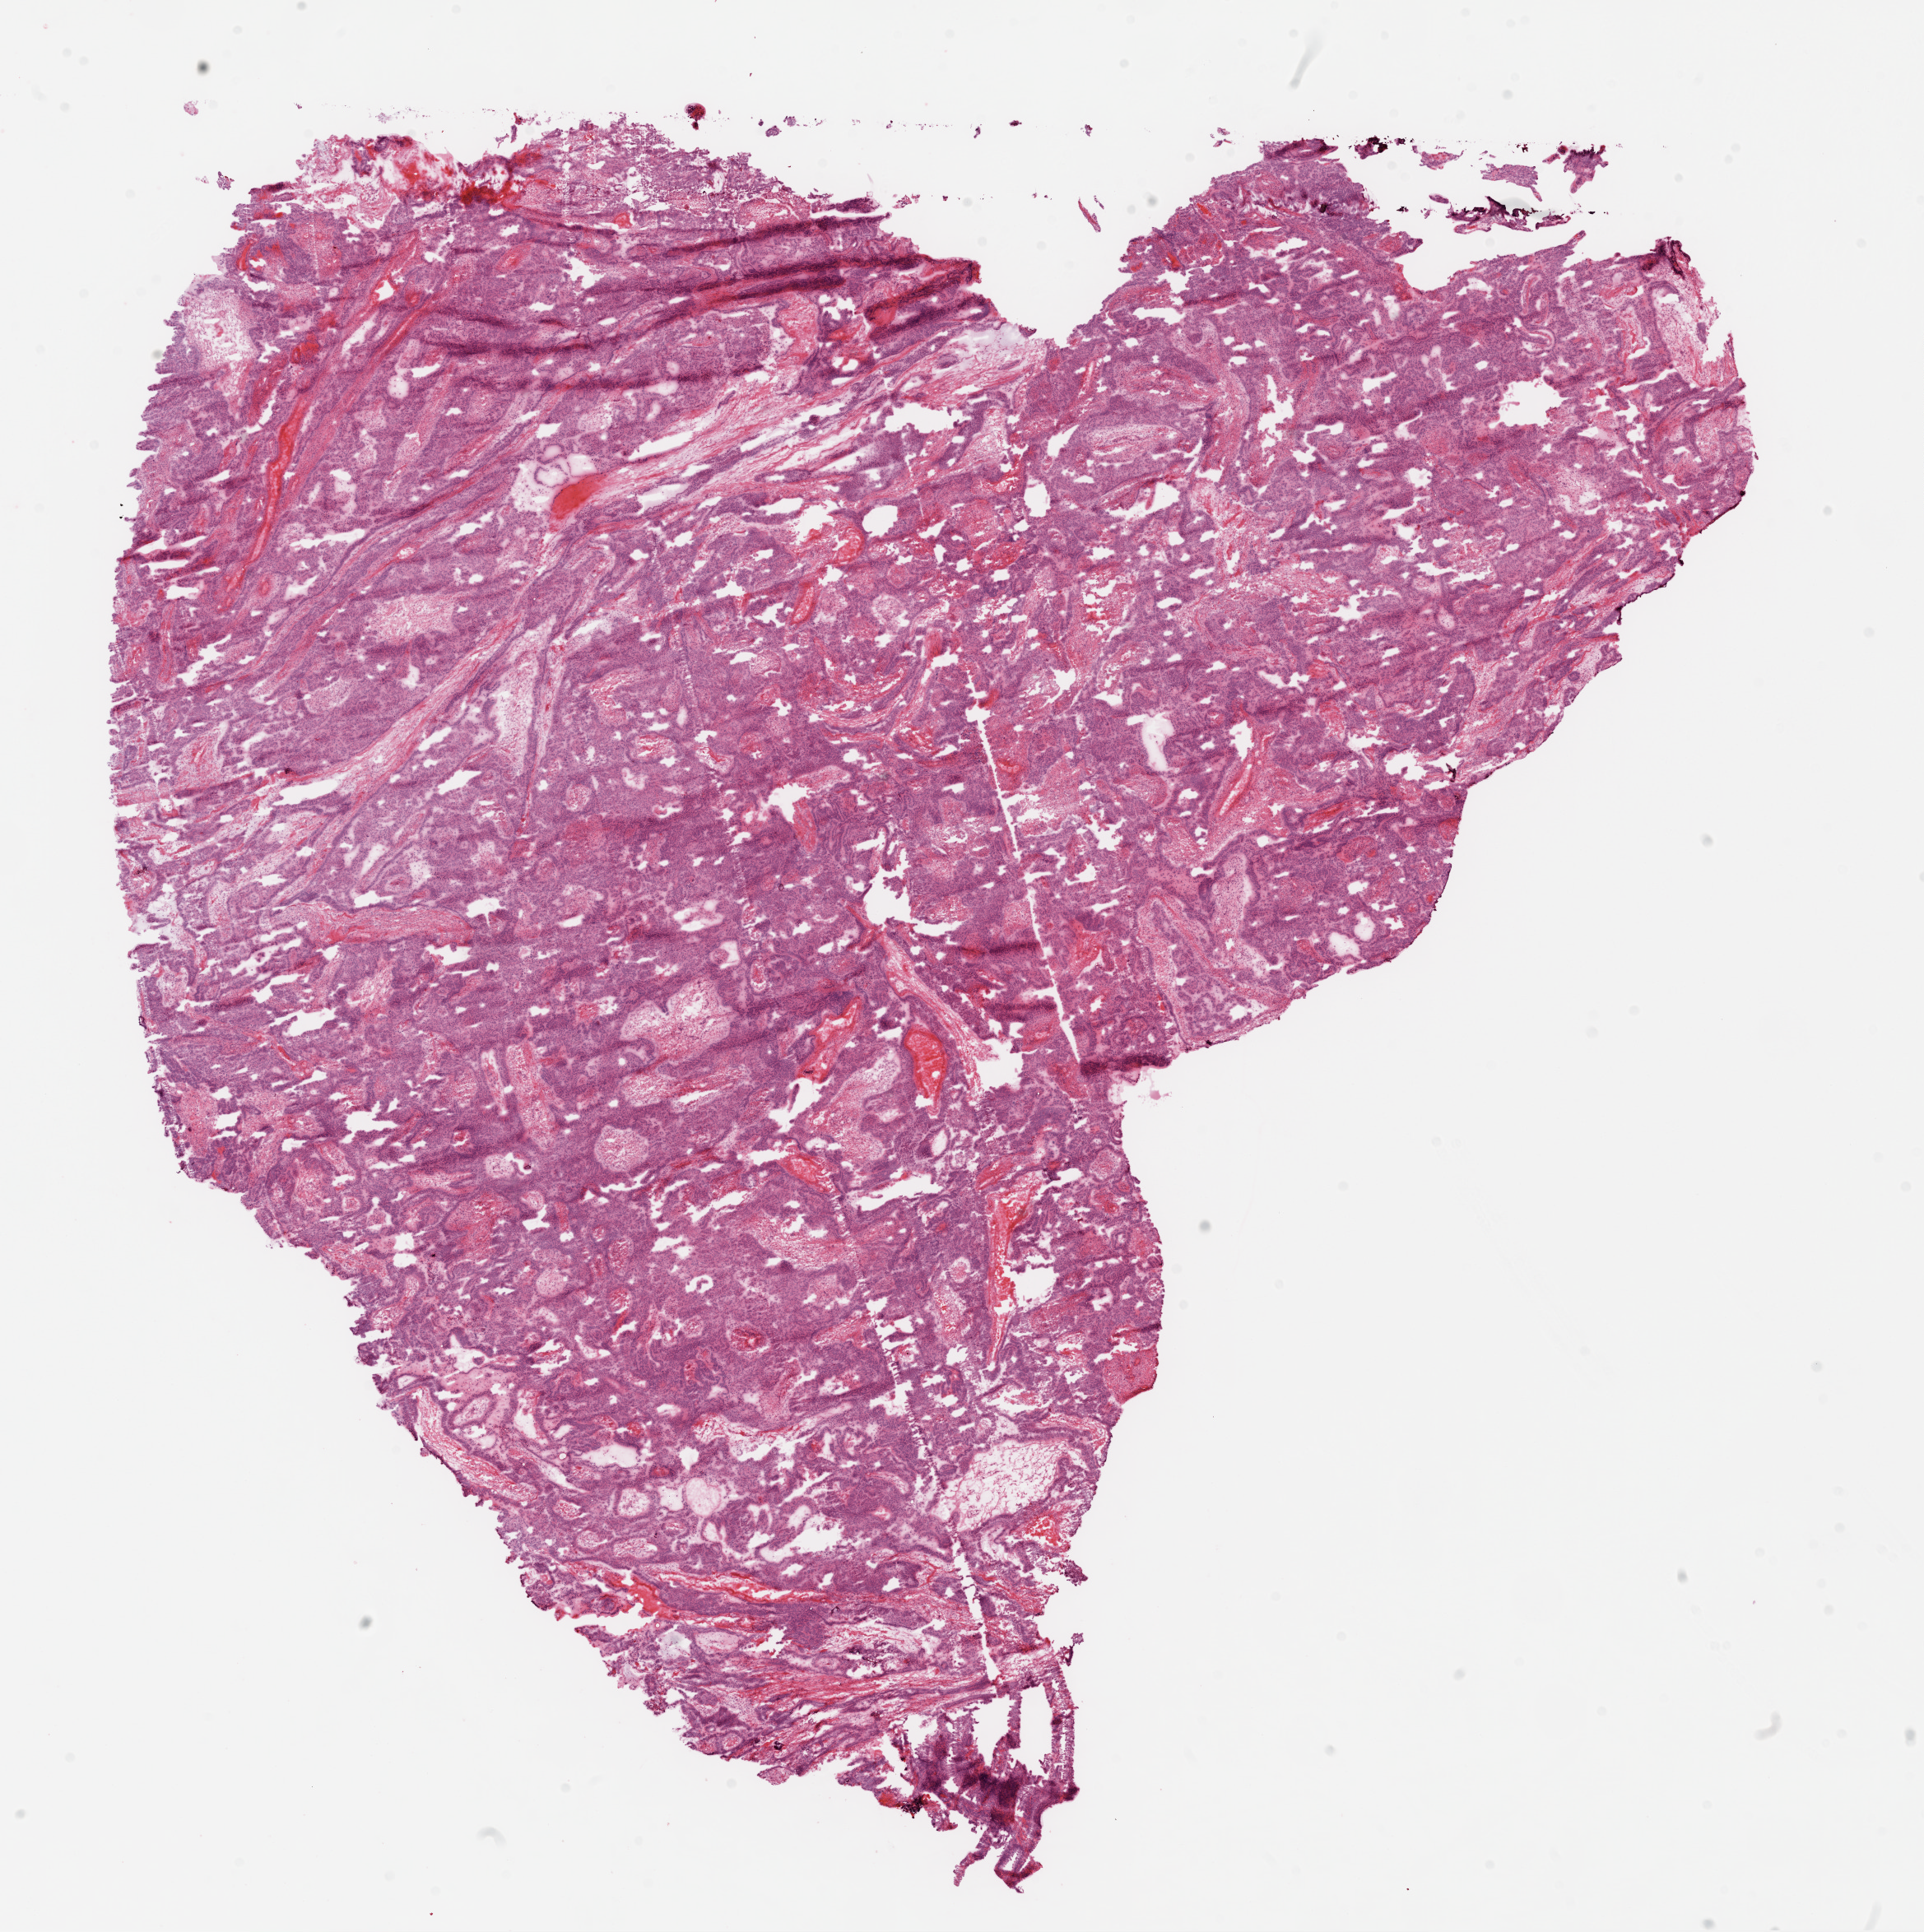
H&E-stained whole-slide image, shown as a low-resolution overview of the whole scanned area (about 18.9 x 18.9 mm, slide scanned at 20x); frozen section from the top of the tissue portion; sample: primary tumour, ovary. Female, age 65 years at initial diagnosis.
Histologic diagnosis: Serous cystadenocarcinoma, NOS.